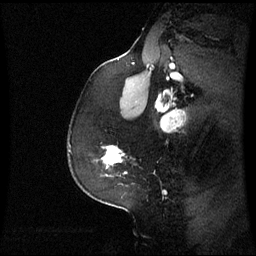
Breast MRI (dynamic contrast-enhanced), one sagittal slice; slice 45 of 60 in the series (ordered by position); dynamic contrast-enhanced series, image 2 of 3 at this slice position (ordered by acquisition); 1.5 T; TE 4.2 ms, TR 8.9 ms; 2.4 mm slice thickness; 256 × 256 image matrix, field of view 230 × 230 mm. Female patient, age 59 years. From the clinical record (not read from this slice): setting: breast cancer imaged before/during neoadjuvant chemotherapy; receptor status: triple-negative.
Annotated regions visible in this slice (semi-automatic segmentation, software-assisted and operator-edited):
- analysis volume of interest (the breast-tissue region the enhancement analysis was run in; not a lesion): bounding box (x1, y1, x2, y2) in pixels: (102, 146, 127, 177)
- tumour enhancement mask (voxels above the 70 % enhancement threshold inside the analysis volume of interest): (103, 146, 121, 165)